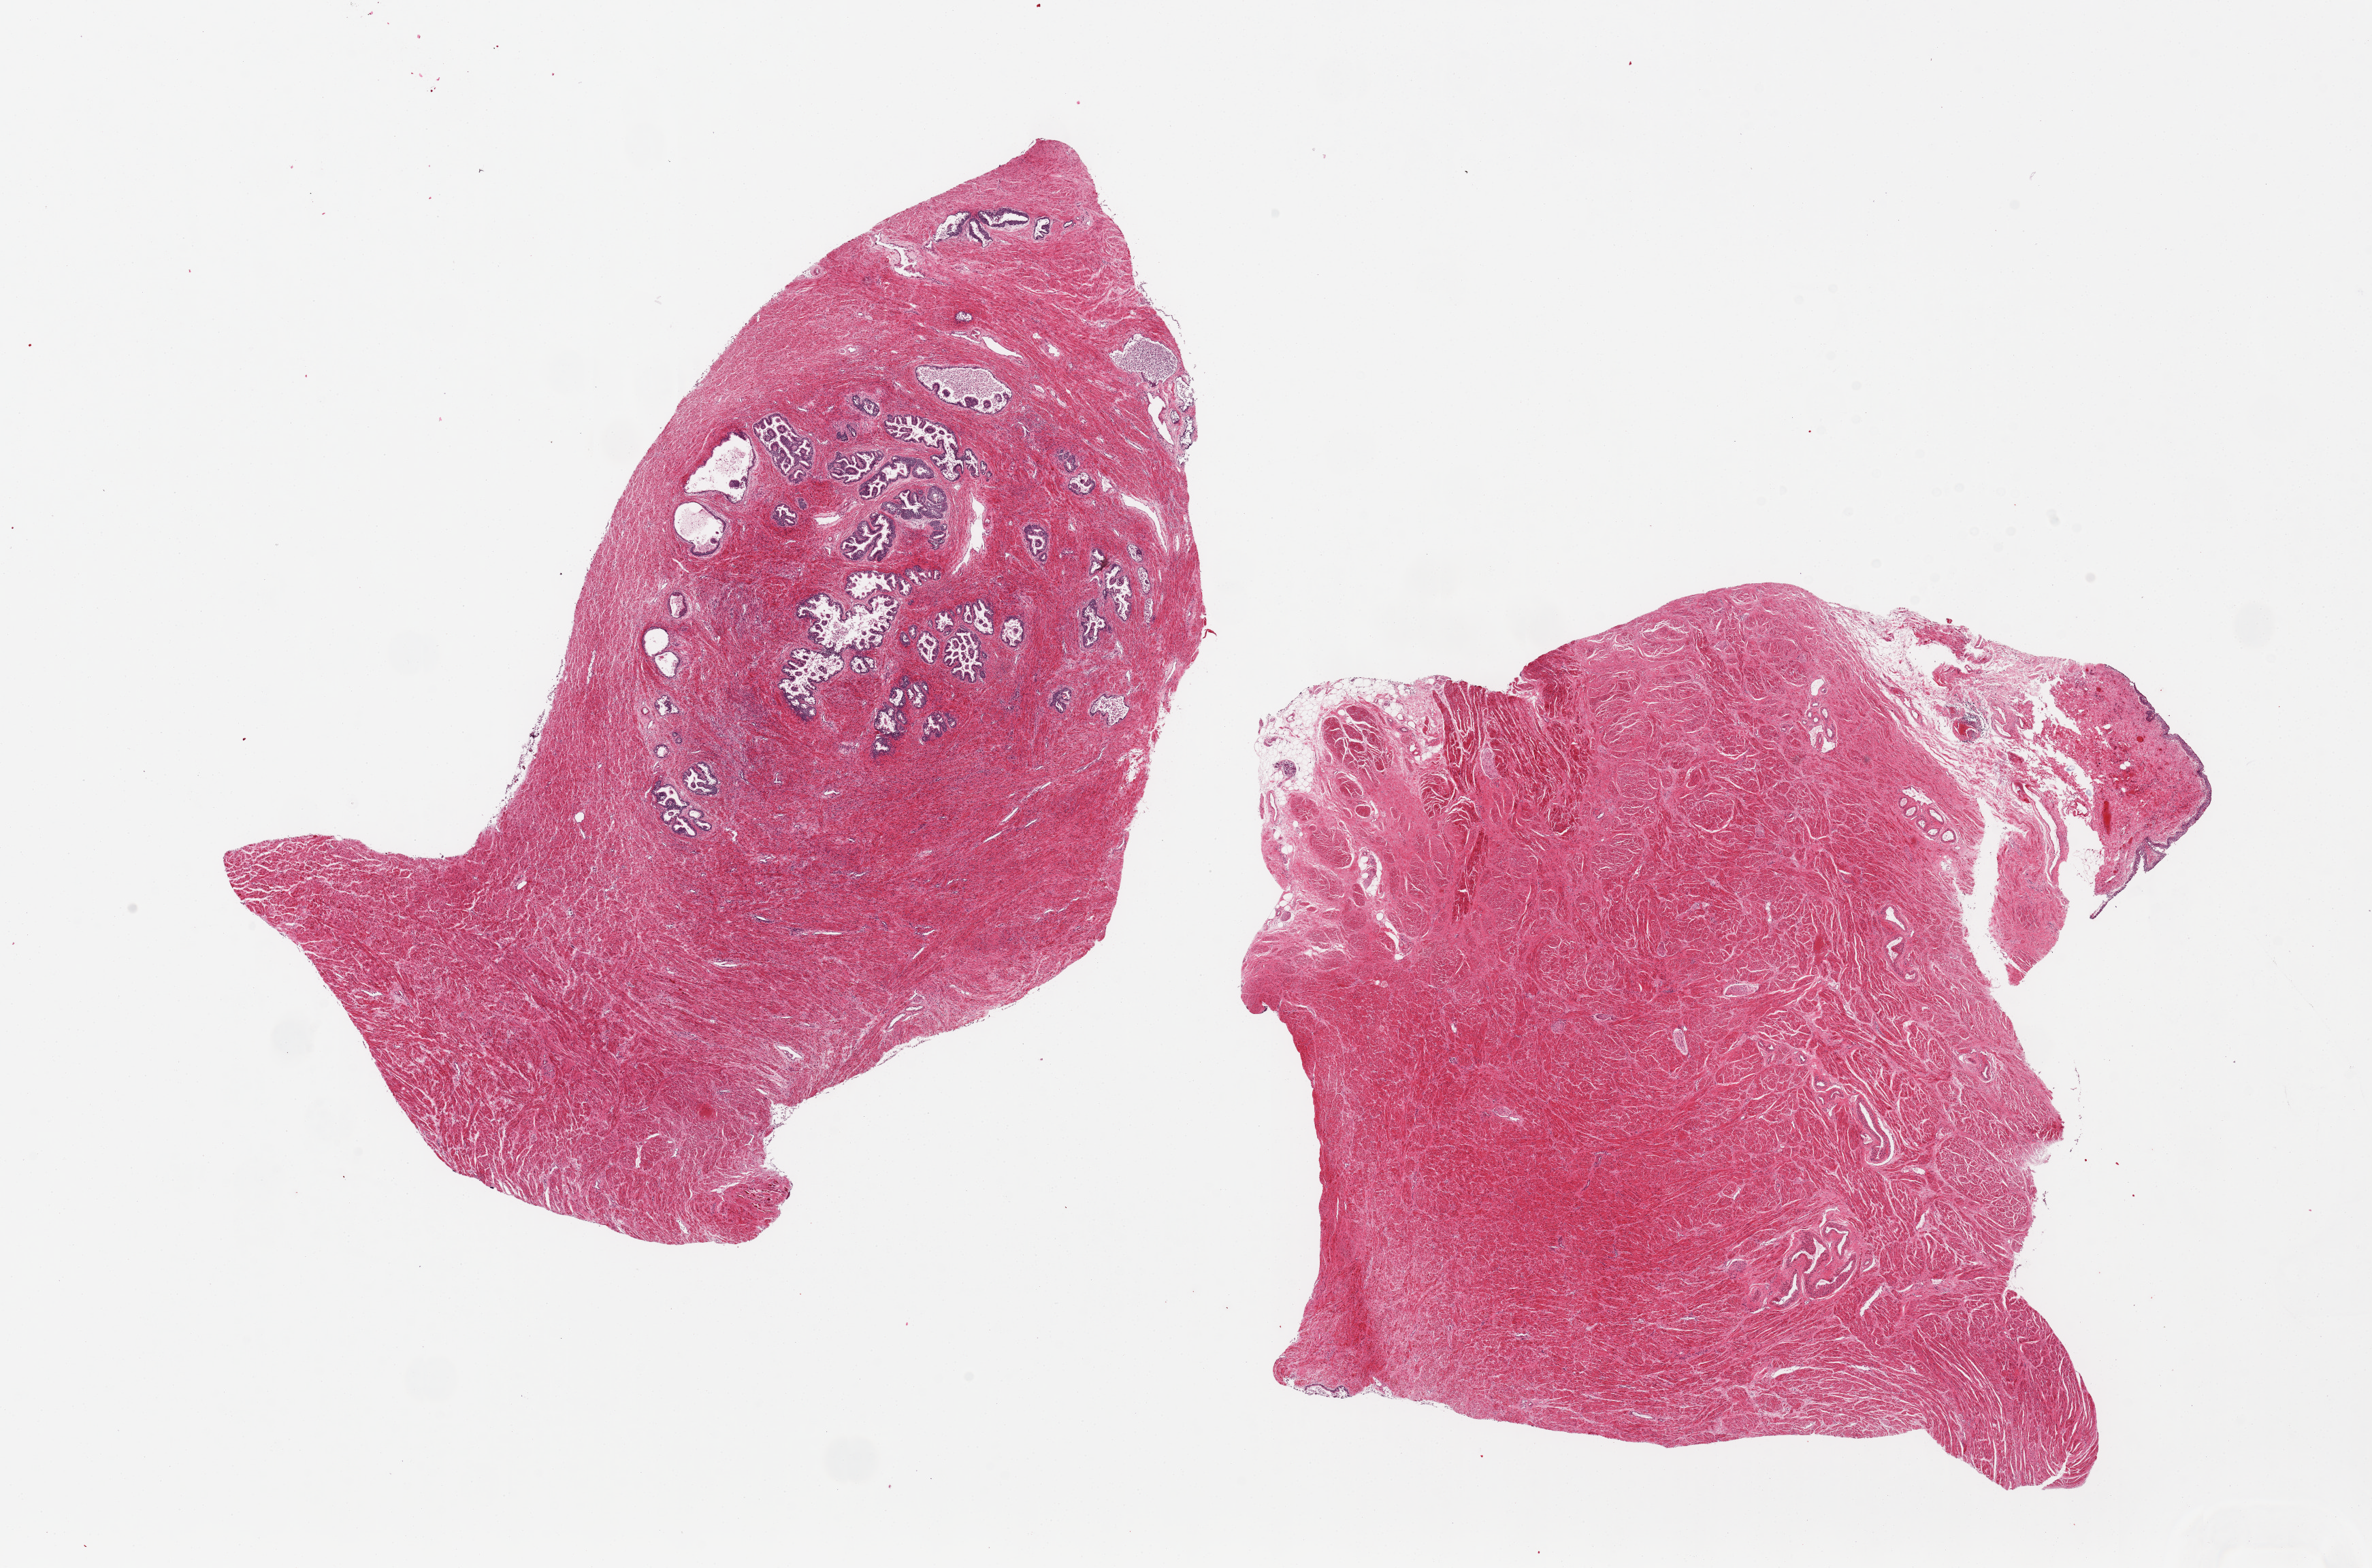
Hematoxylin and eosin (H&E) whole-slide image — shown as a low-resolution overview of the whole scanned area (about 27.6 x 18.2 mm, acquisition: 20x scan). PAXgene-fixed paraffin-embedded (PFPE) section. Target tissue: prostate. Tissue donor sample. Donor sex: male.
Review note (as recorded): 2 pieces, one with nodular hyperplasia, glands comprise ~10%; other with stroma and strip of urothelium.